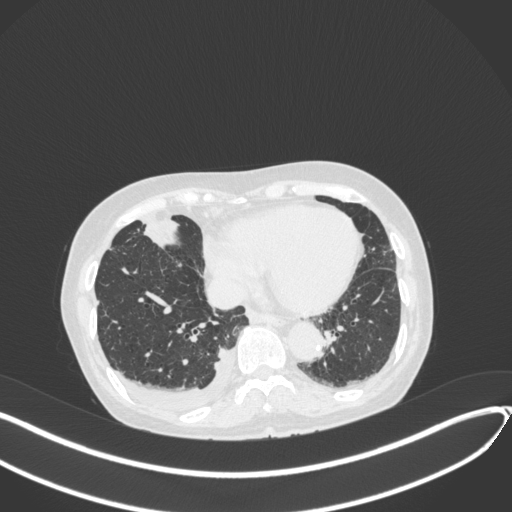
Chest CT, one axial slice. Slice 117 of 418 in the series (ordered by position). Lung window (W 1500 / L -600 HU). 512 × 512 image matrix. Female patient, age 75 years. Case-level facts recorded for this patient, not image findings: clinical TNM (as recorded): T2a N3 M0.
Structures marked on this image (rectangle marked by the reading radiologist):
- lung tumour (recorded histology: adenocarcinoma): bounding box (x1, y1, x2, y2) in pixels: (138, 214, 186, 253)